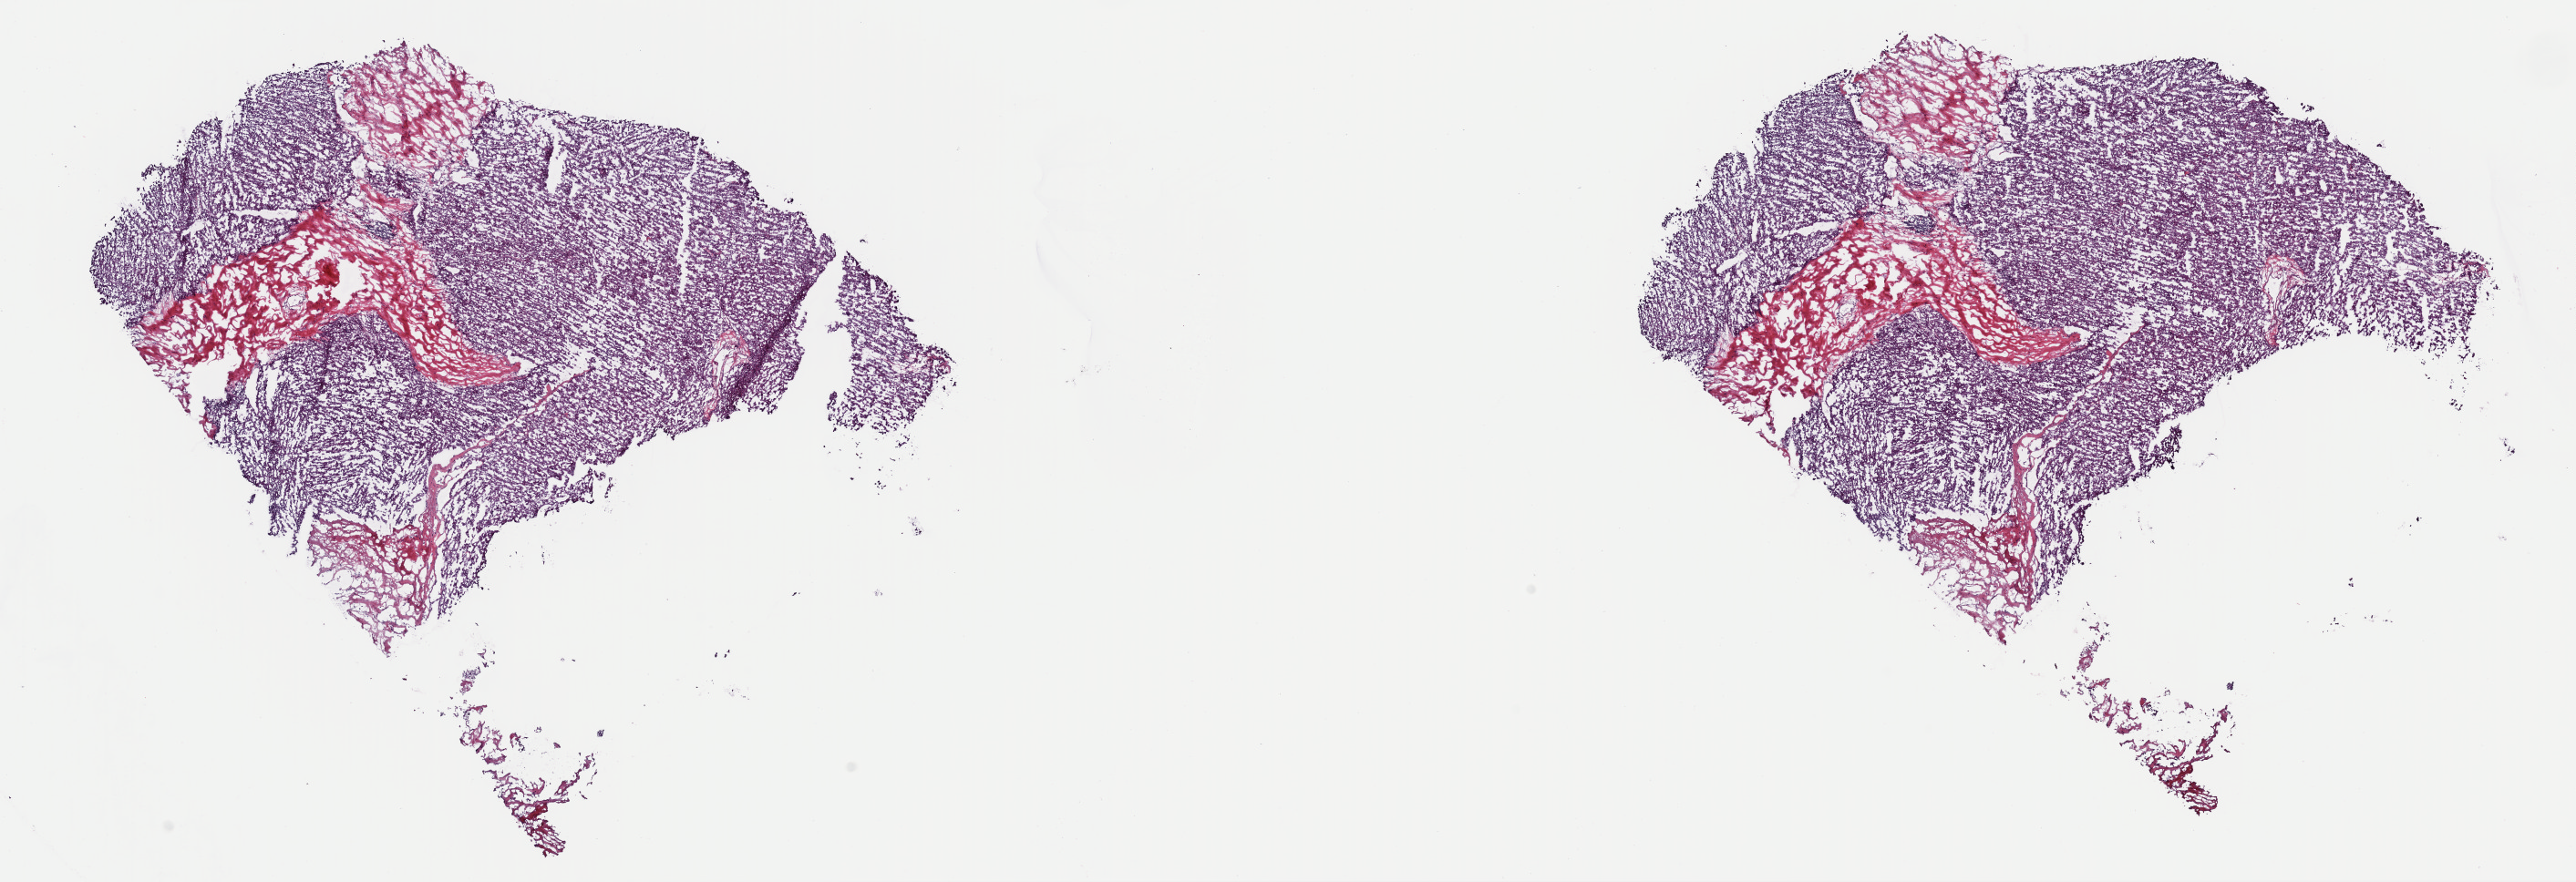
Digitized H&E-stained tissue section (whole slide), a low-resolution overview of the entire scanned area, about 22.3 x 7.6 mm (slide scanned at 40x). Frozen section. Primary tumour sample from the adrenal cortex. Male patient; age at initial diagnosis 62 years. Slide review estimates, as recorded: tumour cells 90%, tumour nuclei 95%.
Diagnosis: Adrenal cortical carcinoma (cortex of adrenal gland).